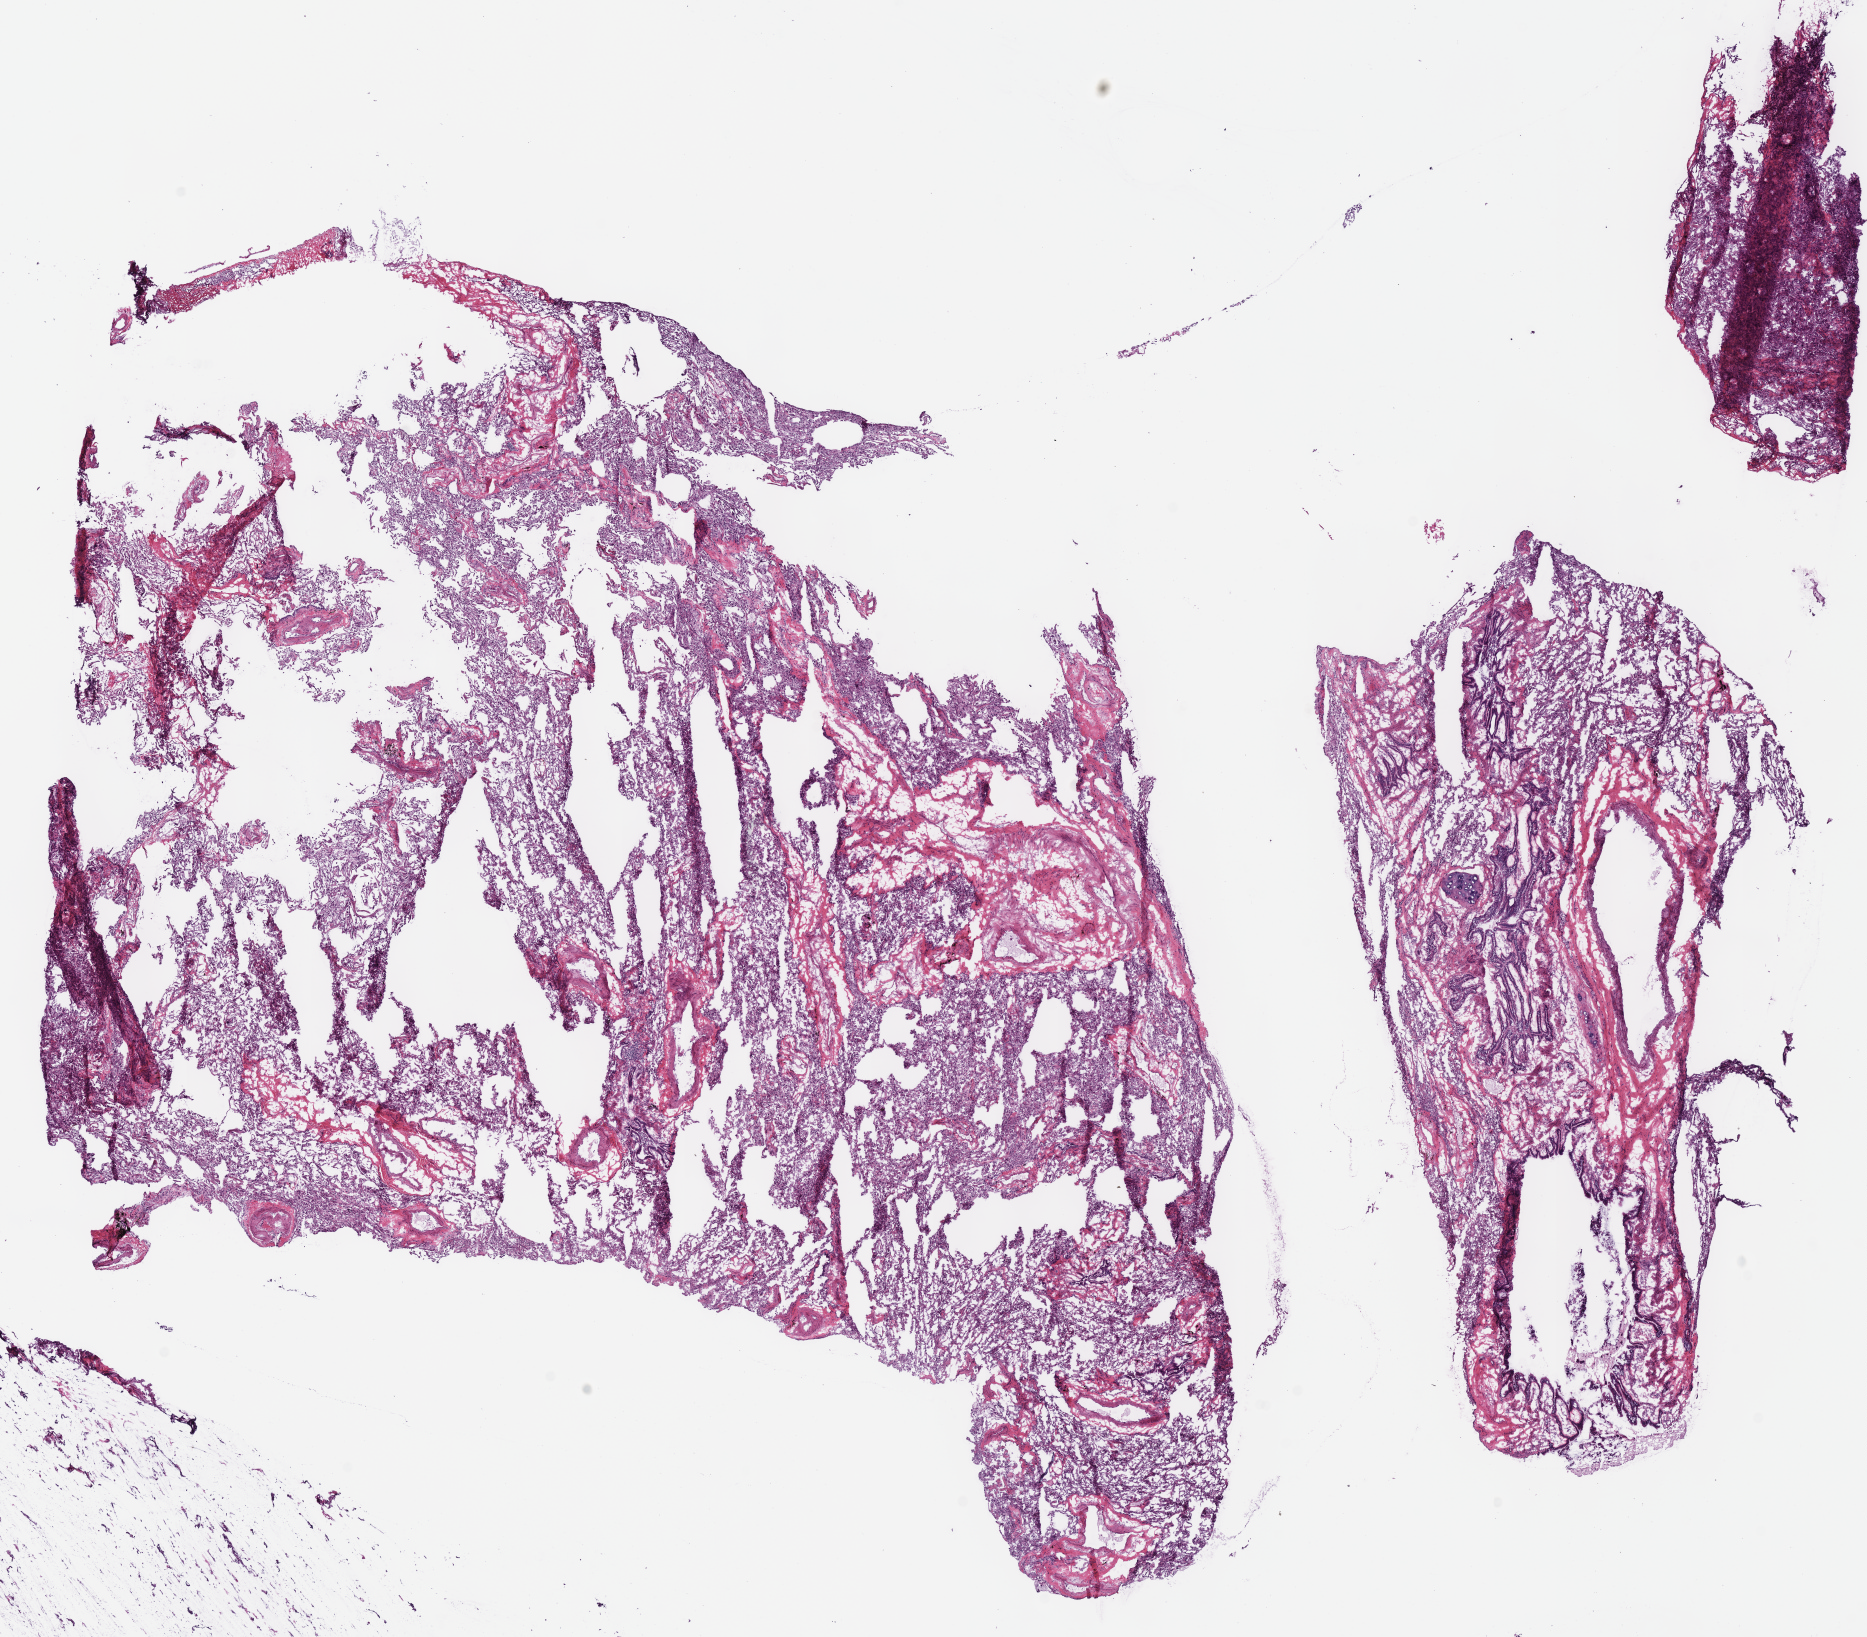
H&E-stained whole-slide image — low-resolution overview of the scanned area, about 14.7 x 12.9 mm (from a 40x scan); frozen section from the top of the tissue portion; solid tissue normal (non-tumour tissue) sample from the lung. Male patient; age at initial diagnosis 70 years.
This section: solid tissue normal (non-tumour) sample from the same patient. Patient diagnosis: Adenocarcinoma, NOS (middle lobe, lung).